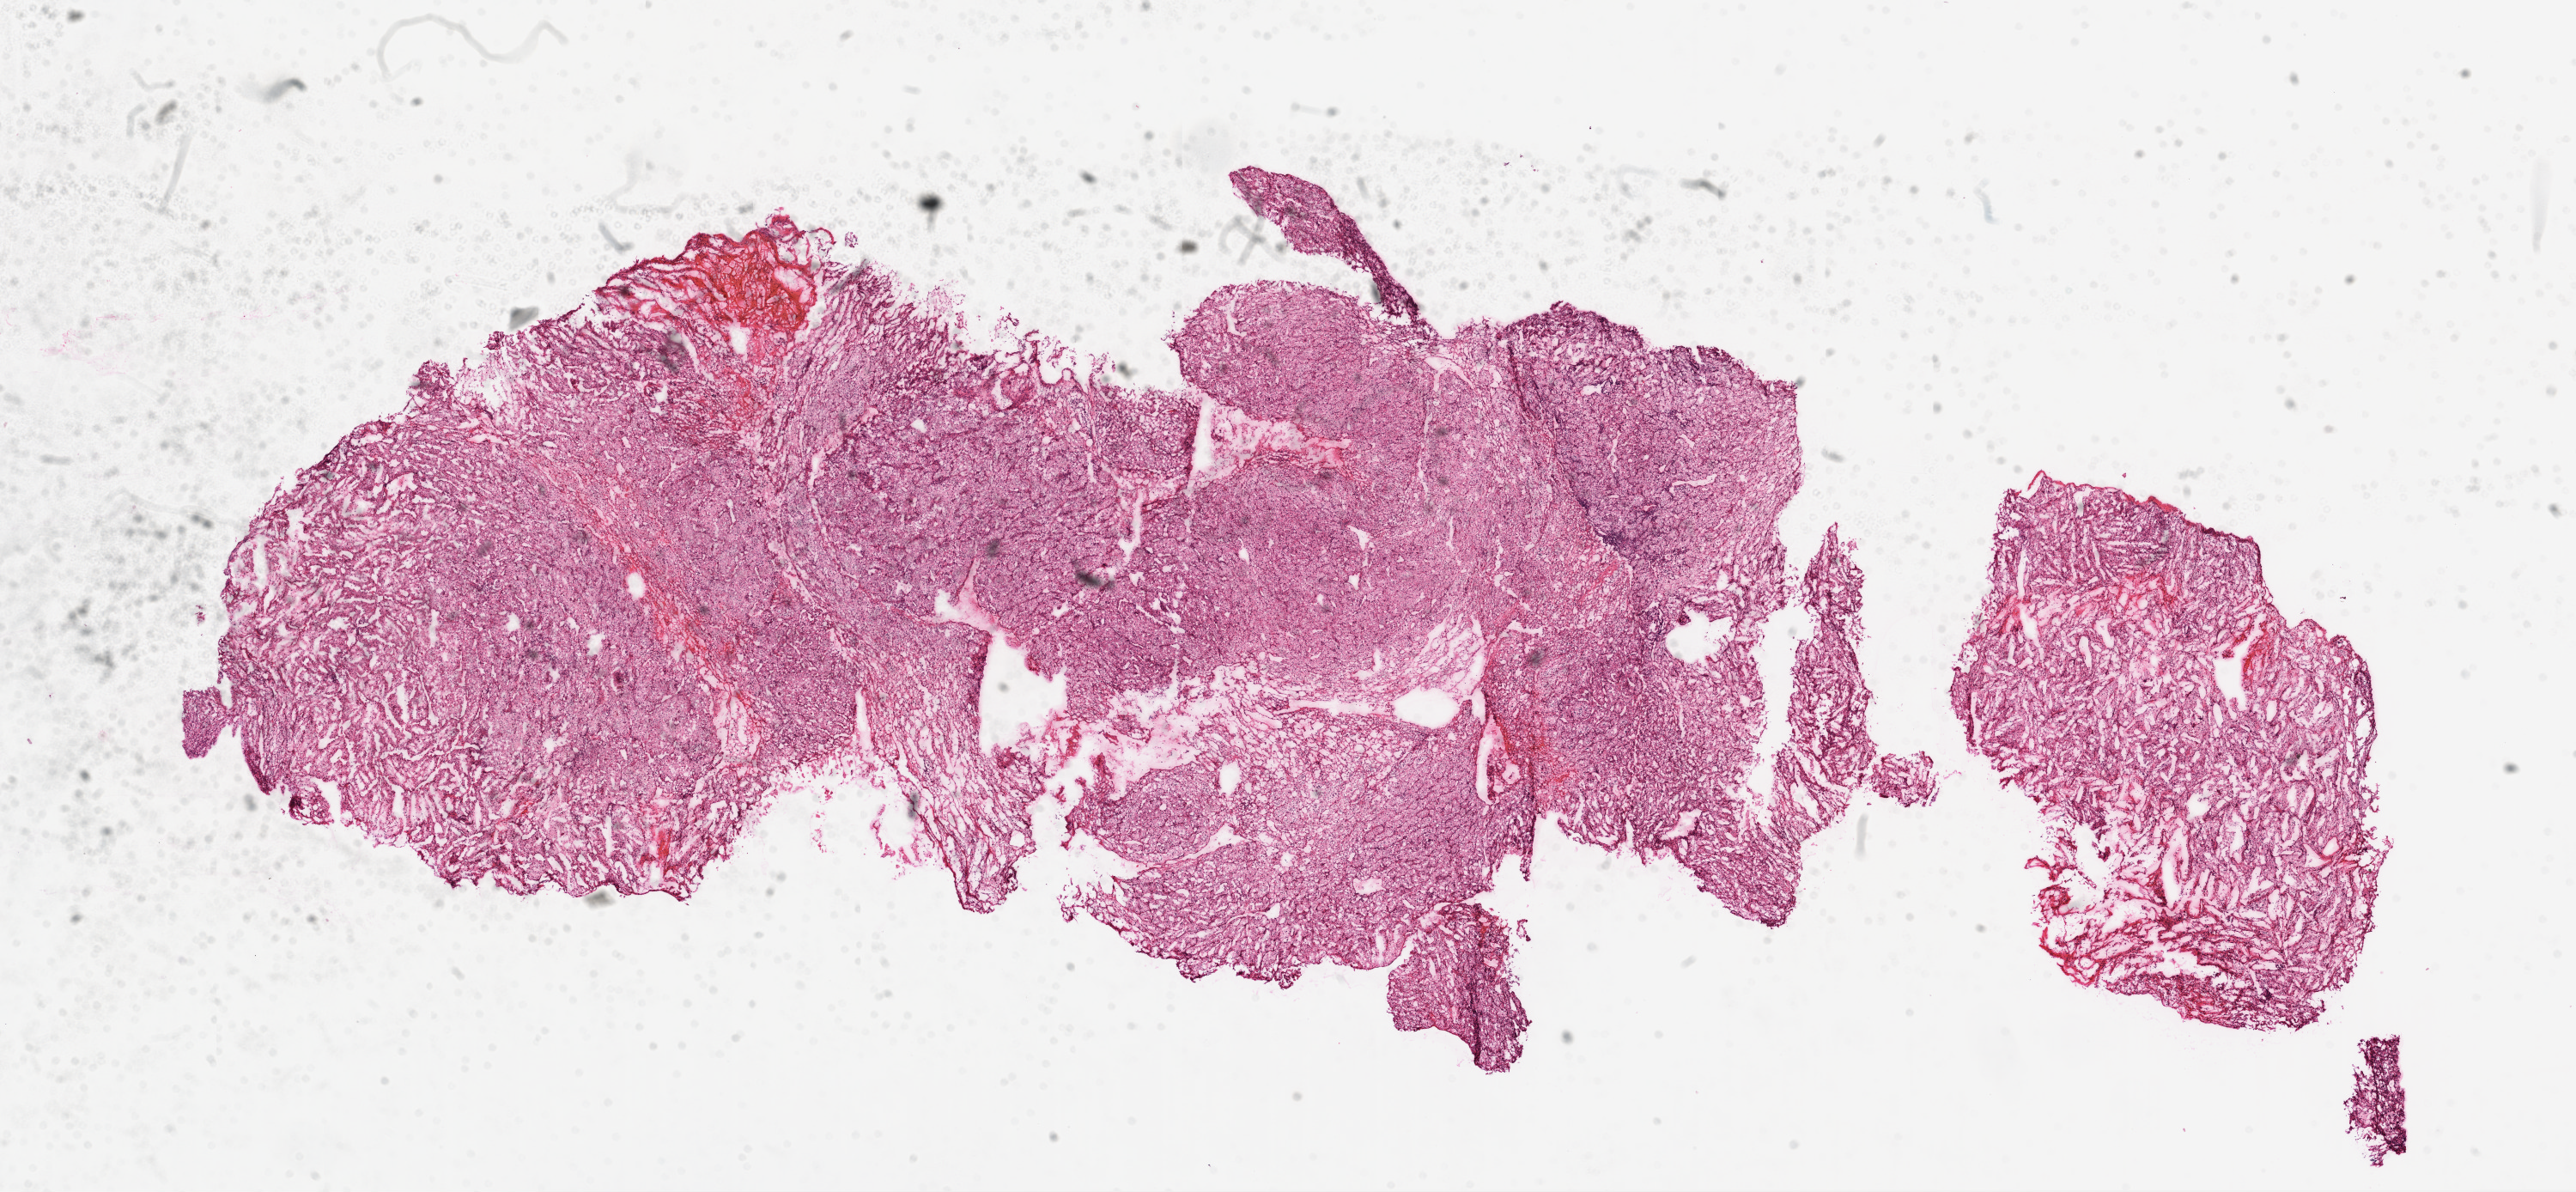
Hematoxylin and eosin (H&E) stained whole-slide image — shown as a low-resolution overview of the whole scanned area (about 24.1 x 11.1 mm); frozen section from the top of the tissue portion; sample: primary tumour, kidney. Female patient; age at initial diagnosis 69 years. Histologic grade: G3 (poorly differentiated). Composition of this section per pathologist review: tumour cells 90%, tumour nuclei 85%, normal cells 0%, stromal cells 10%, necrosis 0%.
Histologic diagnosis: Clear cell adenocarcinoma, NOS. AJCC pathologic stage: III.